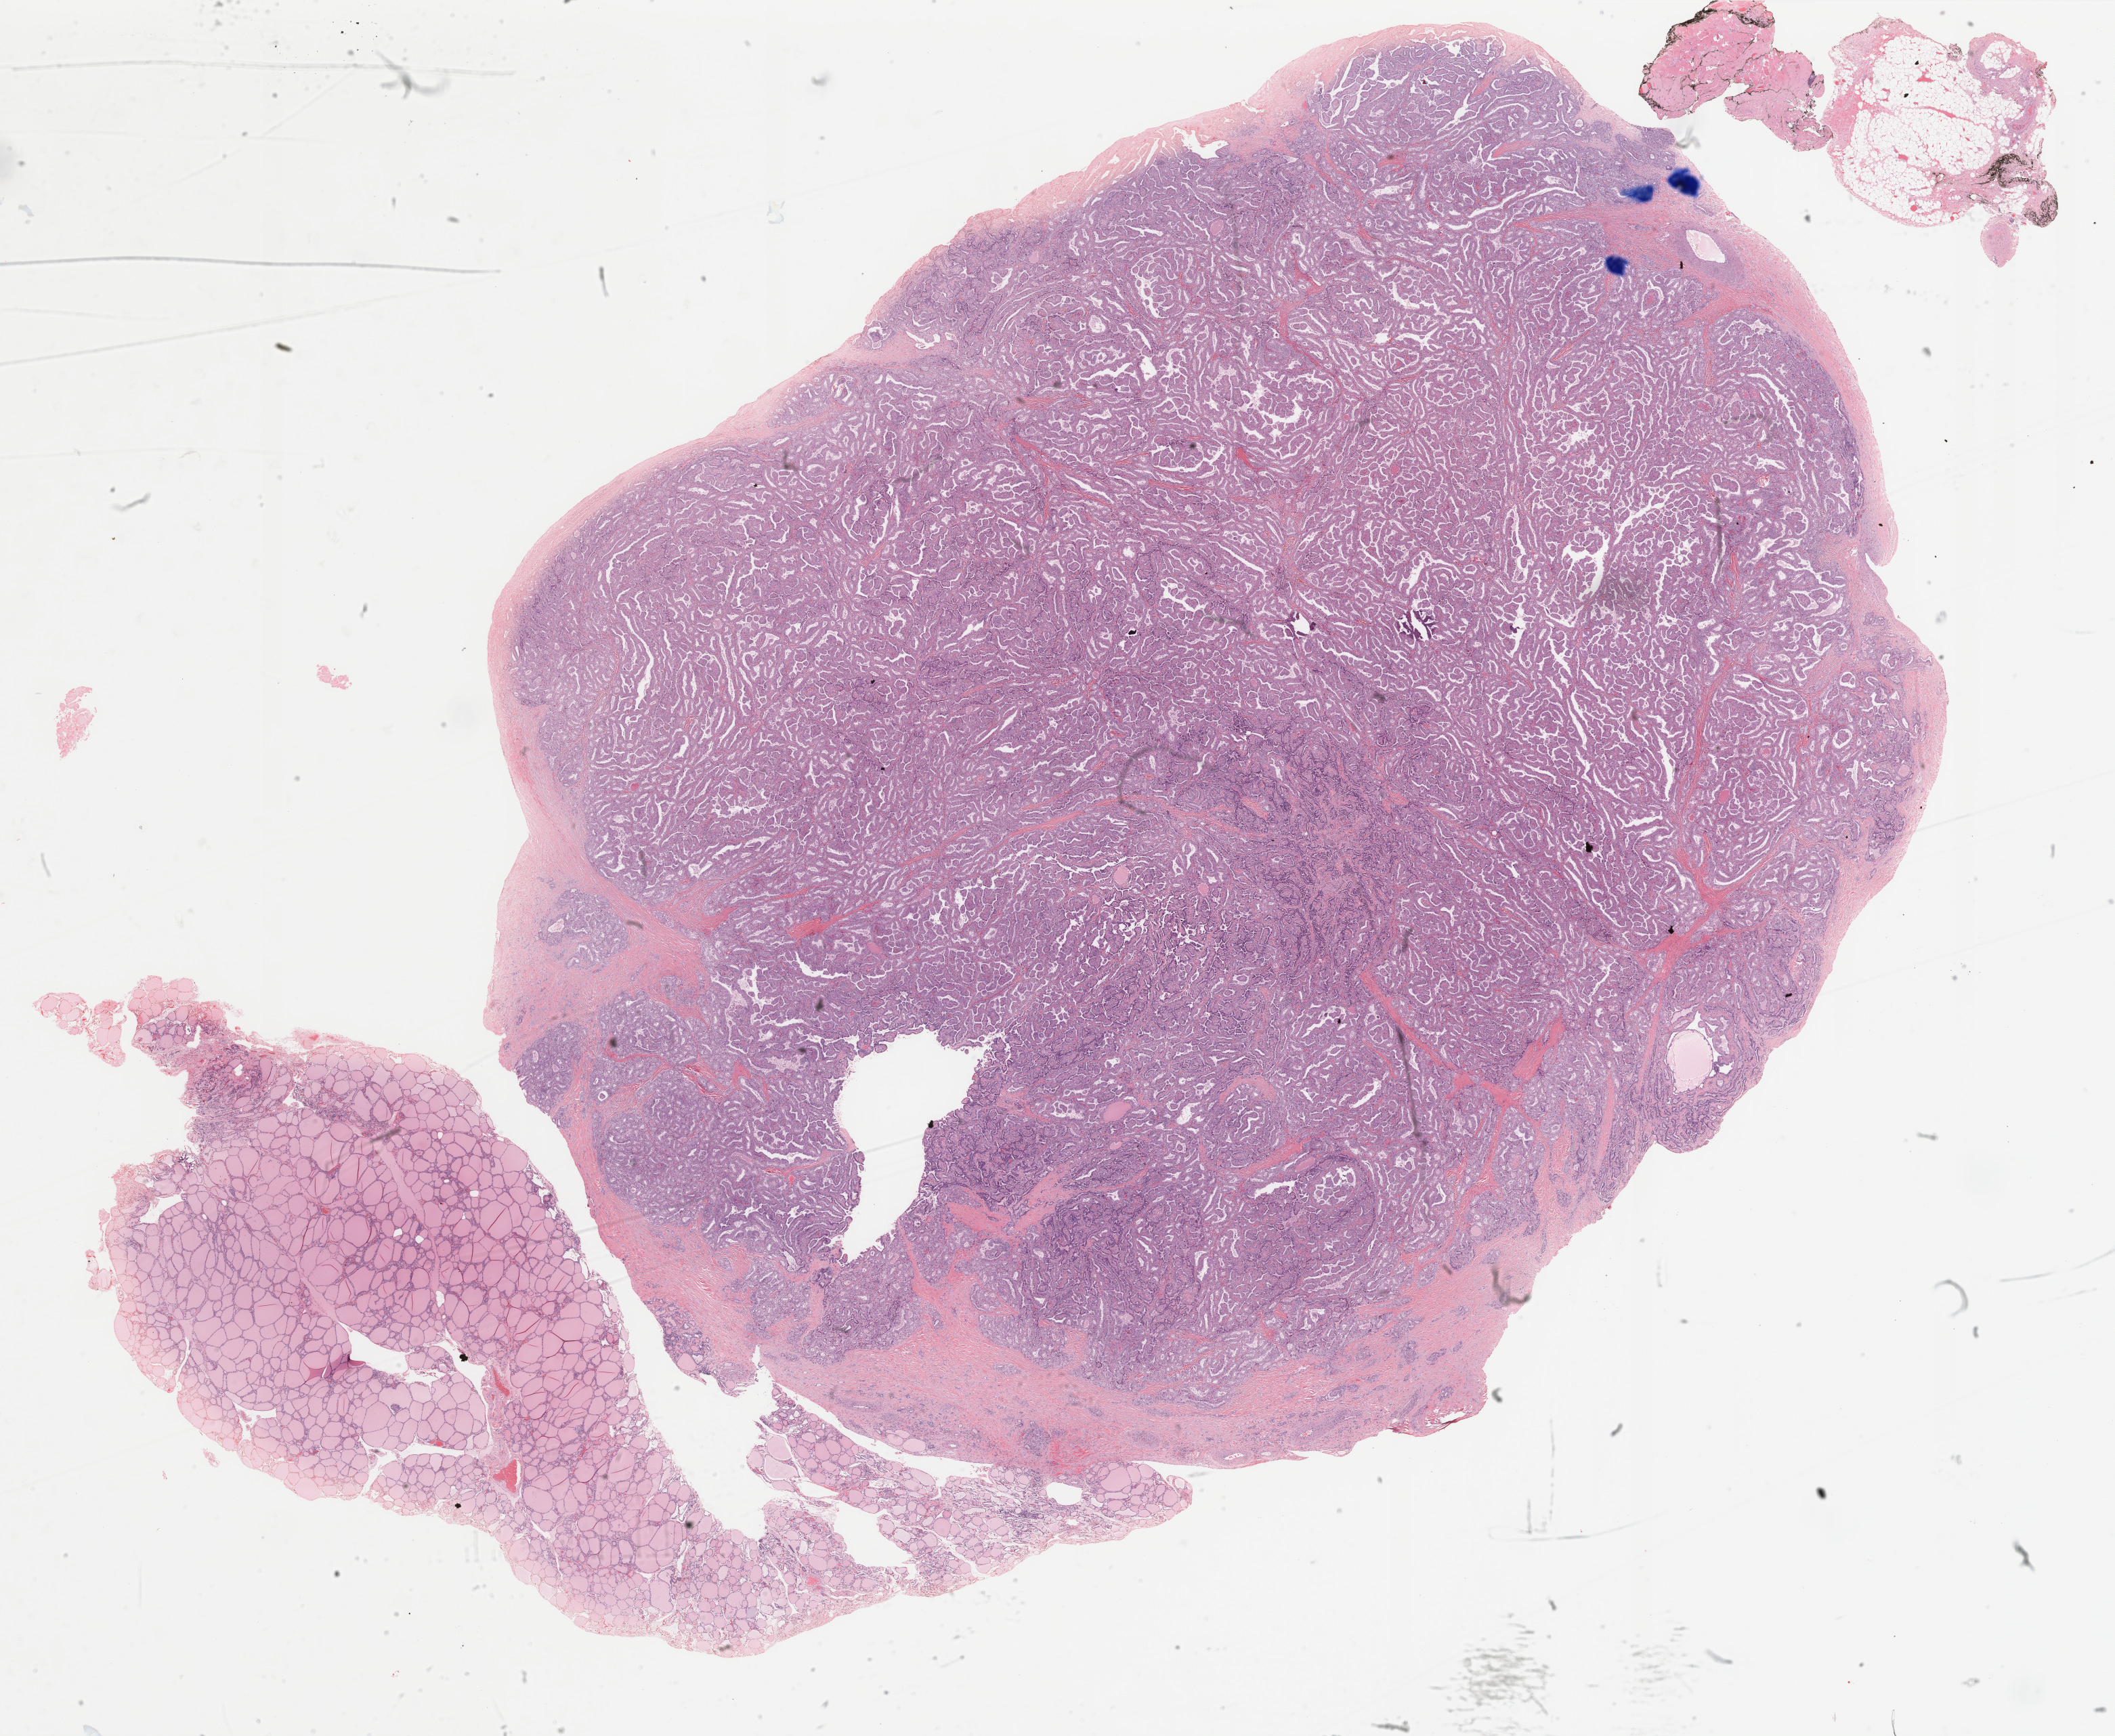
Hematoxylin and eosin (H&E) stained whole-slide image, a low-resolution overview of the entire scanned area, about 24.8 x 20.3 mm (from a 40x scan). Formalin-fixed paraffin-embedded (FFPE) diagnostic section. Primary tumour sample from the thyroid. Female patient; age at initial diagnosis 34 years.
AJCC pathologic stage: I (6th edition). Pathologic diagnosis: Papillary adenocarcinoma, NOS (thyroid gland).